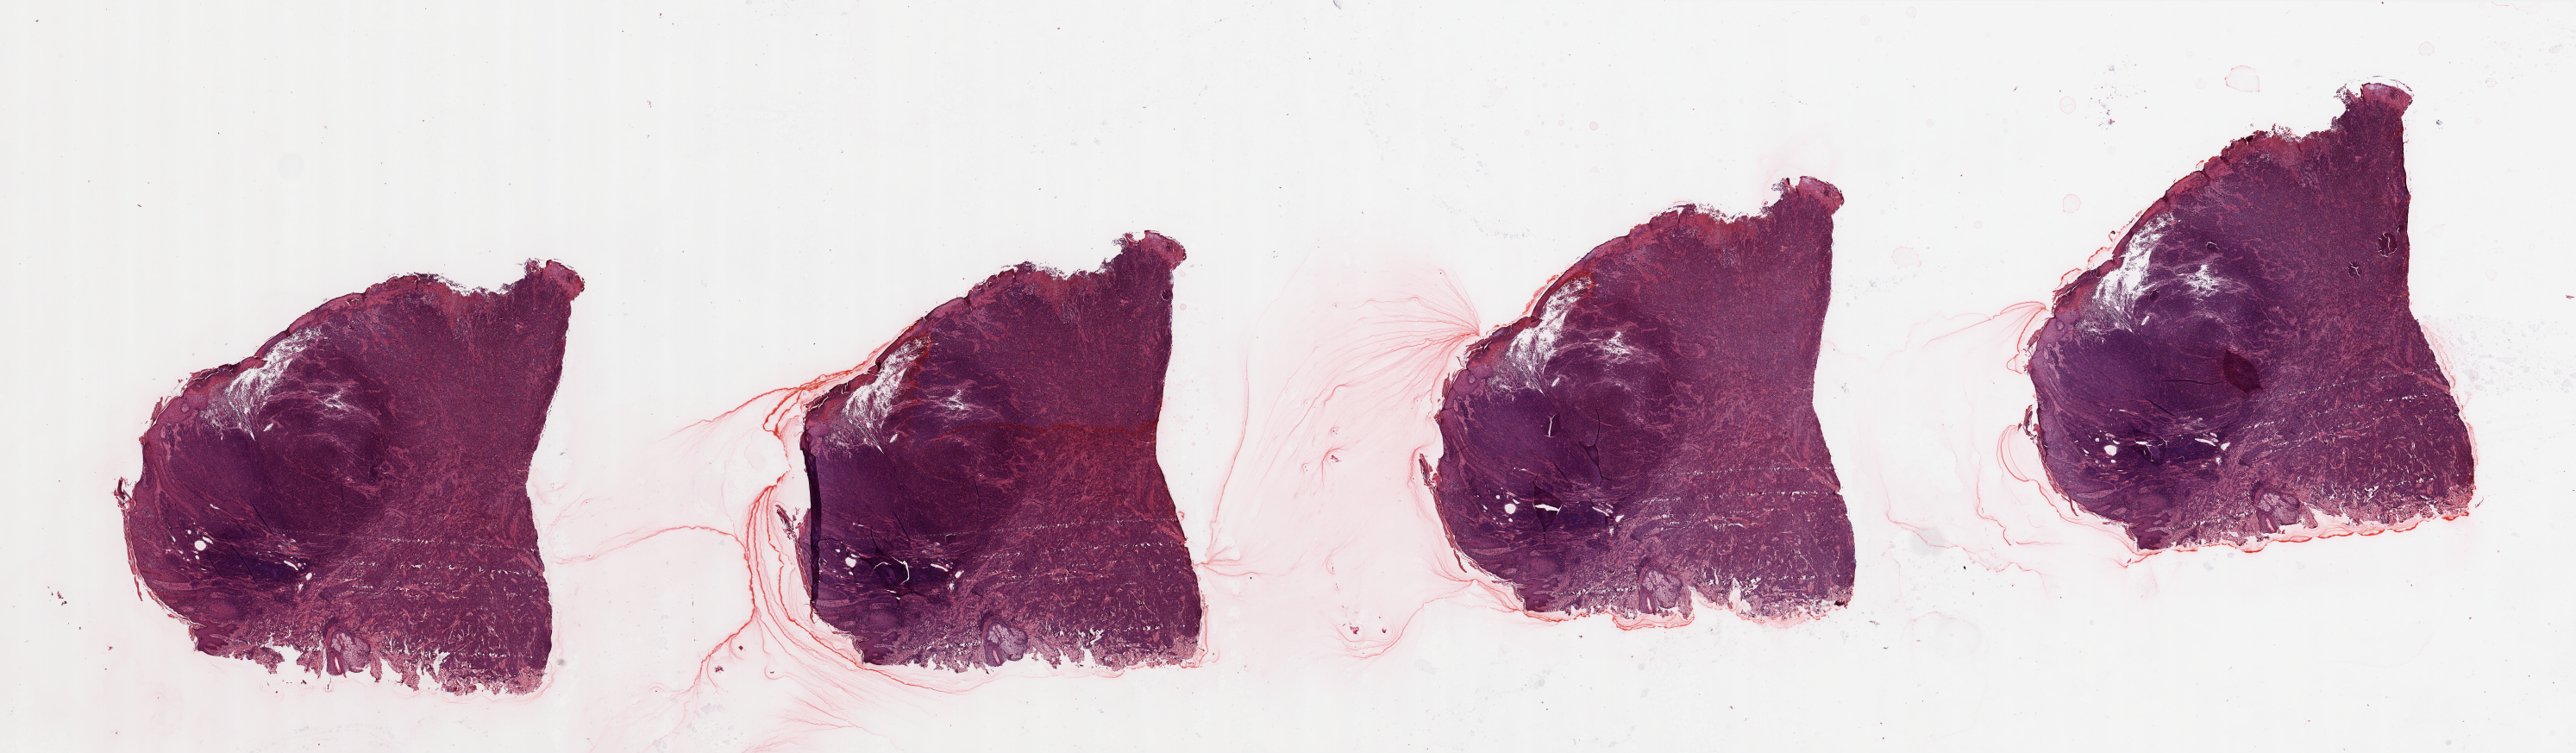
Whole-slide histology image, Hematoxylin and eosin (H&E) stained — shown as a low-resolution overview of the whole scanned area (about 47.3 x 13.8 mm, acquisition: 20x scan); tumour tissue sample, sampled site: trunk. Male, 42 y/o. Pathologist review of this section (percent, as recorded): tumour nuclei 90%, necrosis 0%.
Histologic diagnosis: Malignant melanoma, NOS.